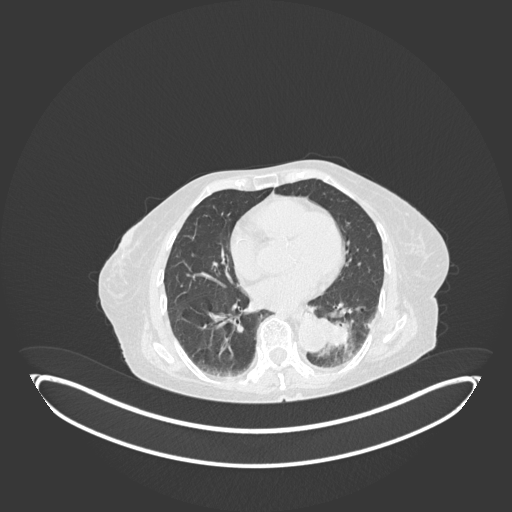
Chest CT, one axial slice. Position 44 of 189 along the scan axis. Reconstruction kernel B30f. 120 kVp. Lung window (W 1500 / L -600 HU). 1 mm slice thickness. 512 × 512 image matrix, field of view 500 × 500 mm. Patient: female, 82 years. From the clinical record (not read from this slice): clinical TNM (as recorded): T1b N0 M1.
Outlined on this slice (rectangle marked by the reading radiologist):
- lung tumour (recorded histology: adenocarcinoma): bounding box [x1, y1, x2, y2] px = [318, 319, 354, 357]